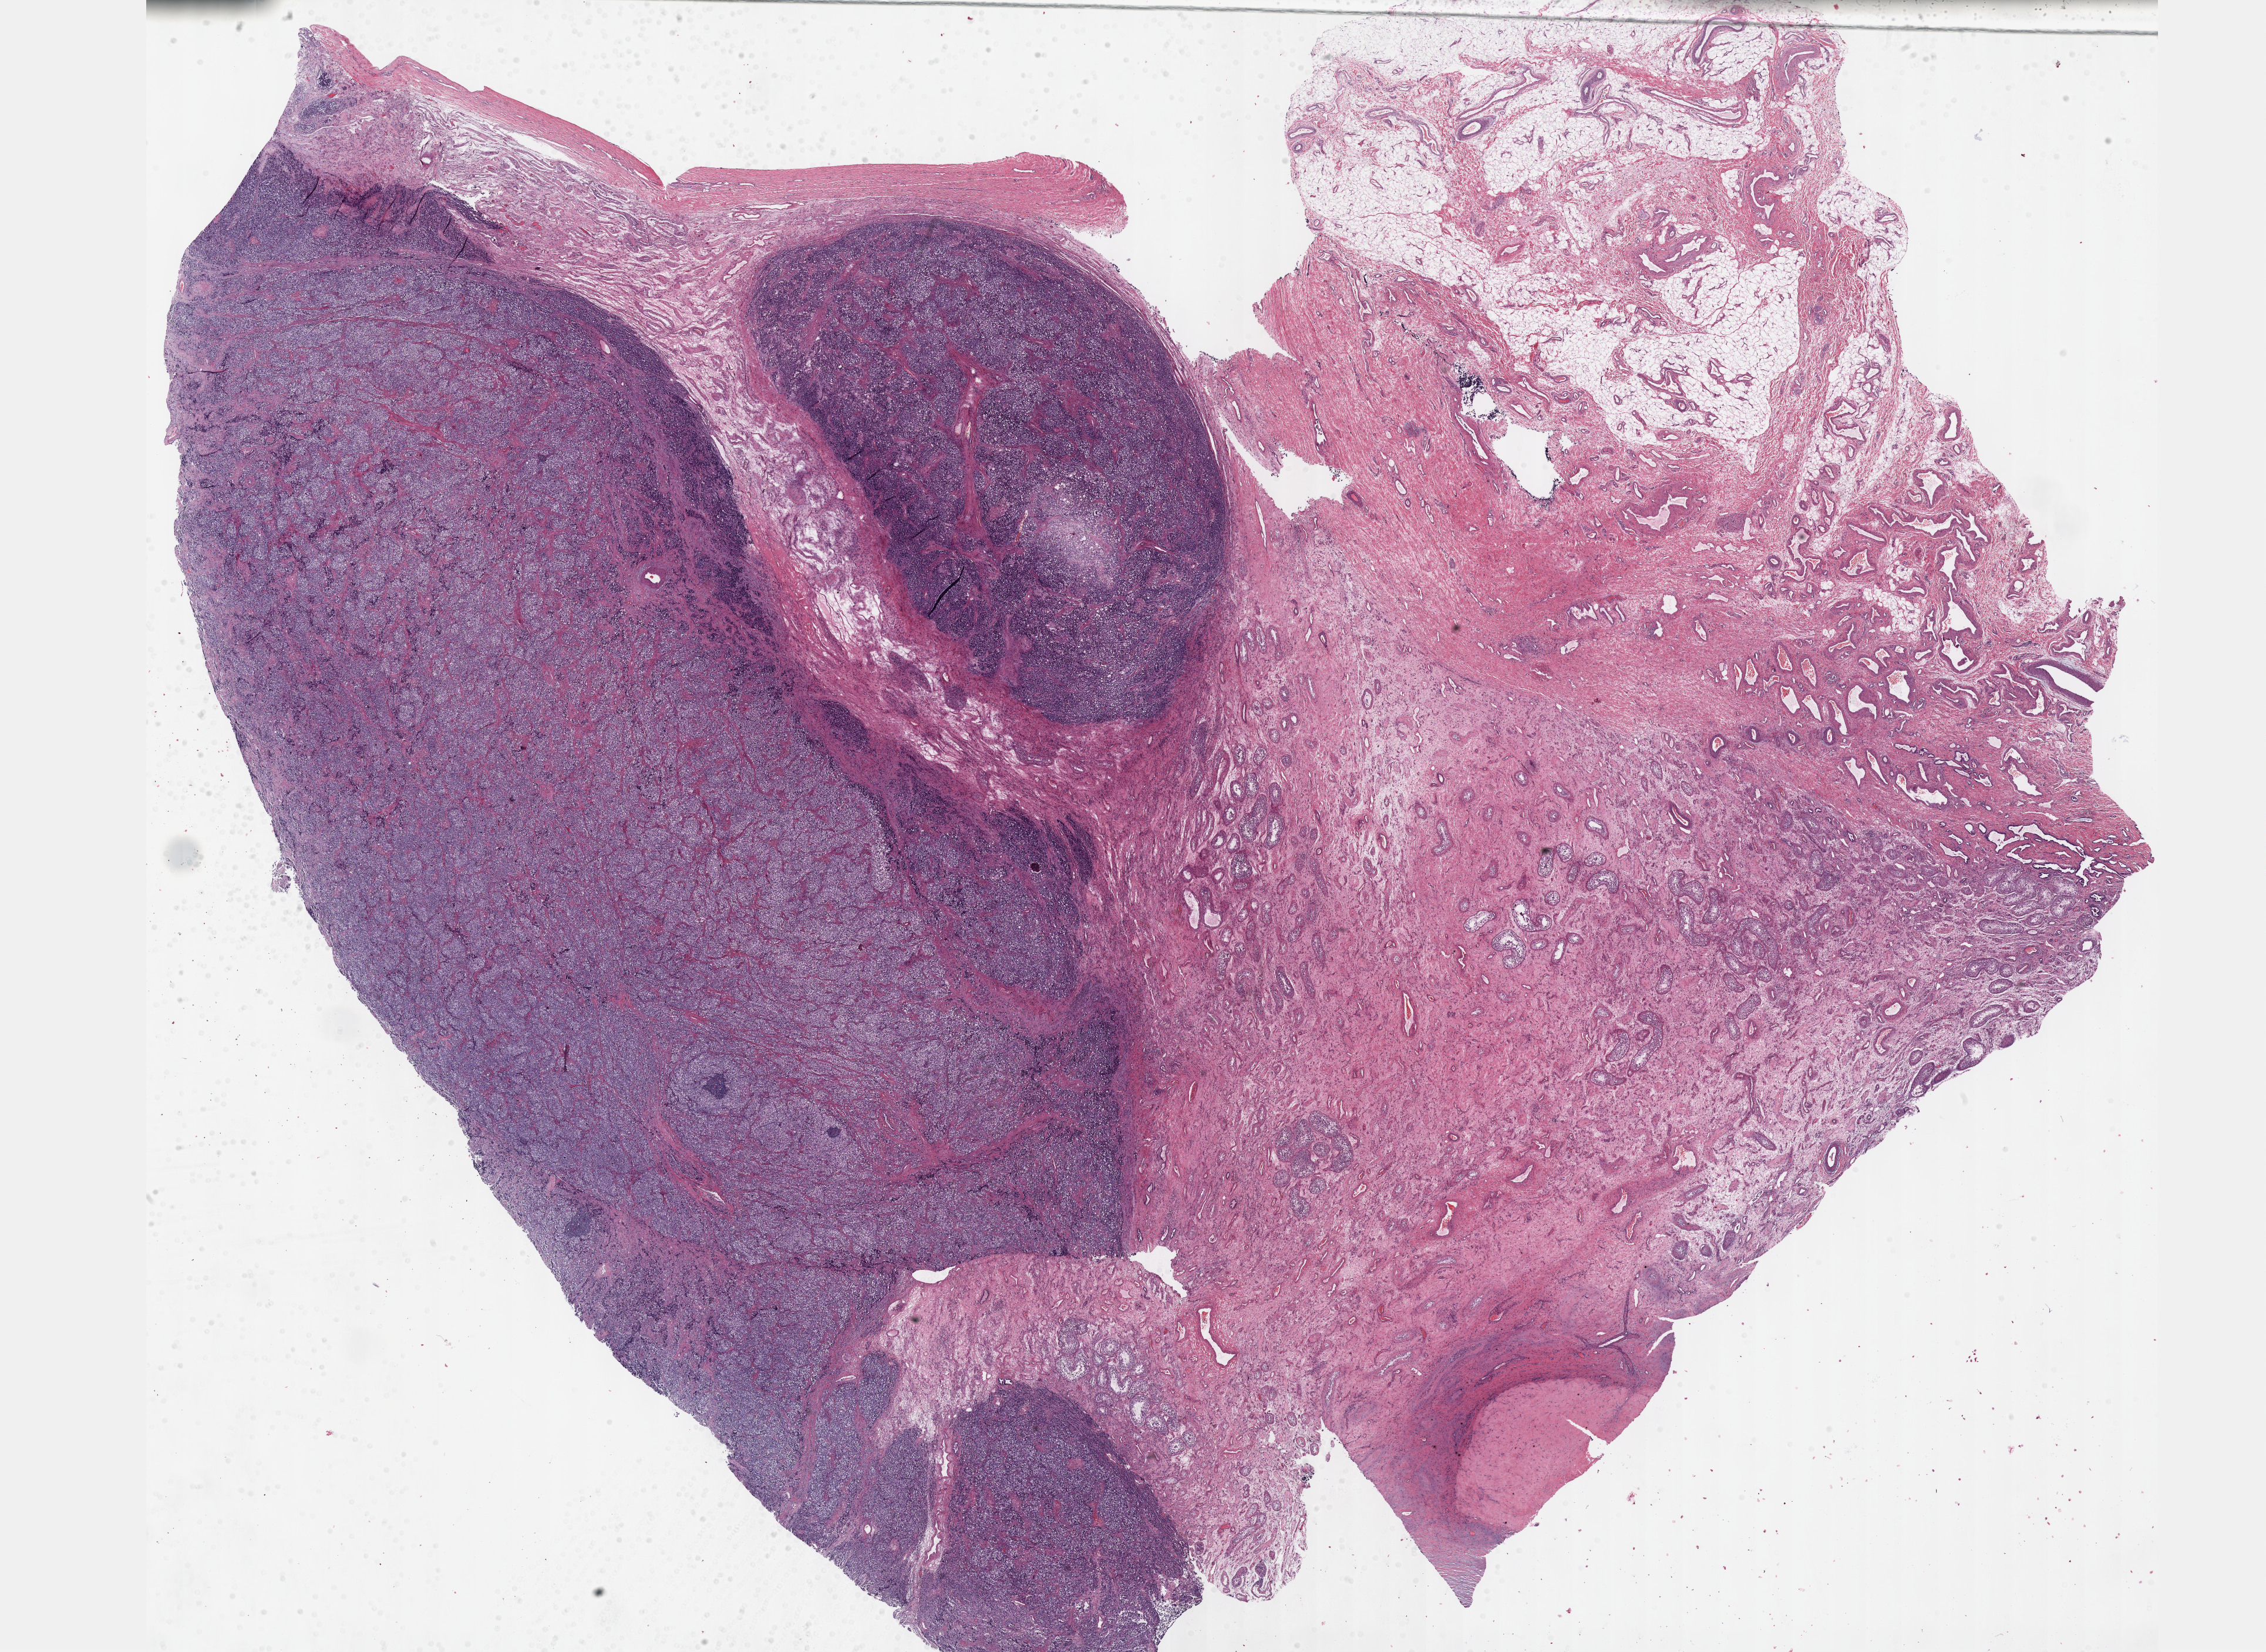
Digitized Hematoxylin and eosin (H&E) stained tissue section (whole slide) — shown as a low-resolution overview of the whole scanned area (about 31.2 x 22.7 mm, from a 40x scan). Formalin-fixed paraffin-embedded (FFPE) diagnostic section. Sample: primary tumour, testis. Patient: male, age at initial diagnosis 27 years.
Histologic diagnosis: Seminoma, NOS.